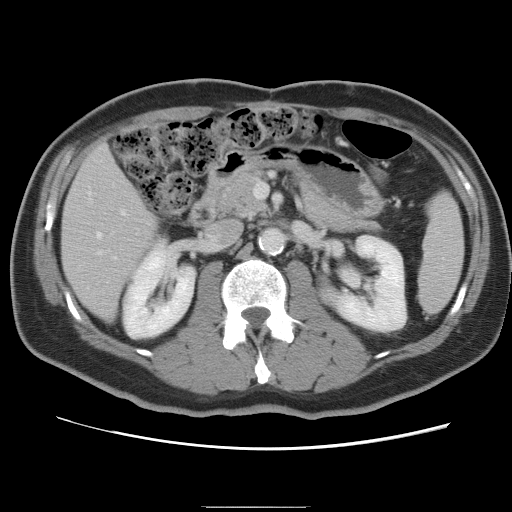
Contrast-enhanced abdominal CT, one axial slice. Slice 35 of 87 in the series (ordered by position). 120 kVp. Intravenous contrast given. Soft-tissue window (W 400 / L 40 HU). 5 mm slice thickness. 512 × 512 image matrix, field of view 363 × 363 mm. Male patient, age 63 years. From the clinical record (not read from this slice): diagnosis: colorectal cancer liver metastases, imaged before liver resection; multiple liver metastases: no; largest metastasis: 9 cm; chemotherapy before resection: no.
Annotated regions visible in this slice (expert manual segmentation):
- hepatic veins: bounding box <97,232,101,237> (left, top, right, bottom; pixels)
- liver: <62,144,158,320>
- planned liver remnant (the part of the liver to remain after resection): <62,144,158,320>
- portal vein (with intrahepatic branches): <112,208,127,260>